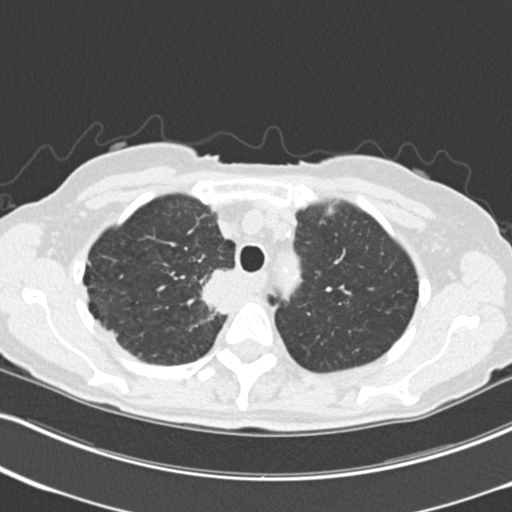
Low-dose screening chest CT, one axial slice. Slice 178 of 226 in the series (ordered by position). Lung window (W 1500 / L -600 HU). 2 mm slice thickness. 512 × 512 image matrix.
Structures marked on this image (outlined manually by an expert reader):
- lesion 1 (tumor, mediastinum): bounding box [x1, y1, x2, y2] px = [202, 270, 233, 314]